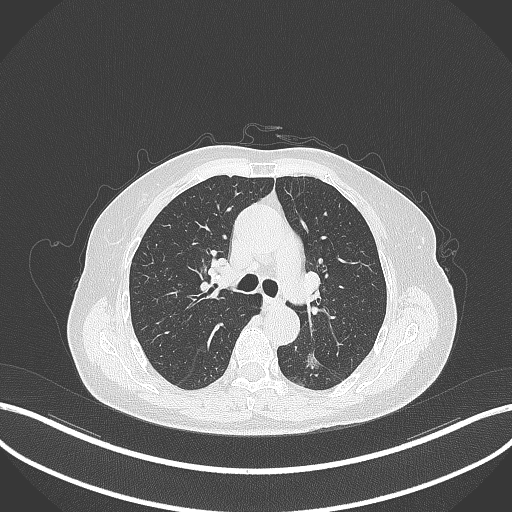
Chest CT, one axial slice; position 197 of 352 along the scan axis; reconstruction kernel B70f; 120 kVp; lung window (W 1500 / L -600 HU); 1 mm slice thickness; 512 × 512 image matrix, field of view 400 × 400 mm. Patient: female, 70 years. From the clinical record (not read from this slice): clinical TNM (as recorded): T1c N0 M0.
Structures marked on this image (rectangle marked by the reading radiologist):
- lung tumour (recorded histology: adenocarcinoma): box from (x=301, y=340) to (x=323, y=377) px